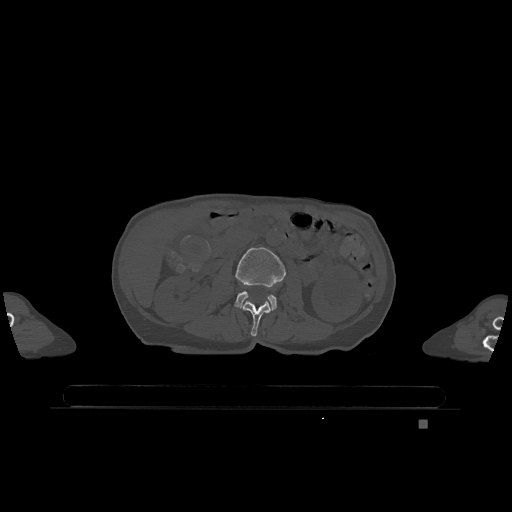
CT including the spine, one axial slice; position 386 of 1317 along the scan axis; bone window (W 1800 / L 400 HU); 0.5 mm slice thickness; 512 × 512 image matrix, field of view 500 × 500 mm. Patient: female, 74 years. Case-level facts recorded for this patient, not image findings: primary cancer: lung.
Outlined on this slice (semi-automatic segmentation, software-assisted and operator-edited):
- L2 vertebra: box from (x=243, y=301) to (x=271, y=337) px
- L3 vertebra: (x=234, y=247)–(x=286, y=311)